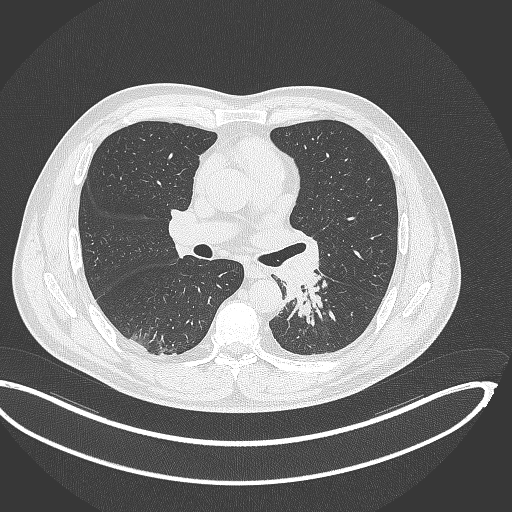
Chest CT, one axial slice. Slice 200 of 362 in the series (ordered by position). 120 kVp. Lung window (W 1500 / L -600 HU). 512 × 512 image matrix, field of view 442 × 442 mm. Male patient, age 50 years. From the clinical record (not read from this slice): clinical TNM (as recorded): T2a N3 M0.
Outlined on this slice (rectangle marked by the reading radiologist):
- lung tumour (recorded histology: squamous cell carcinoma): bounding box <279,267,331,323> (left, top, right, bottom; pixels)